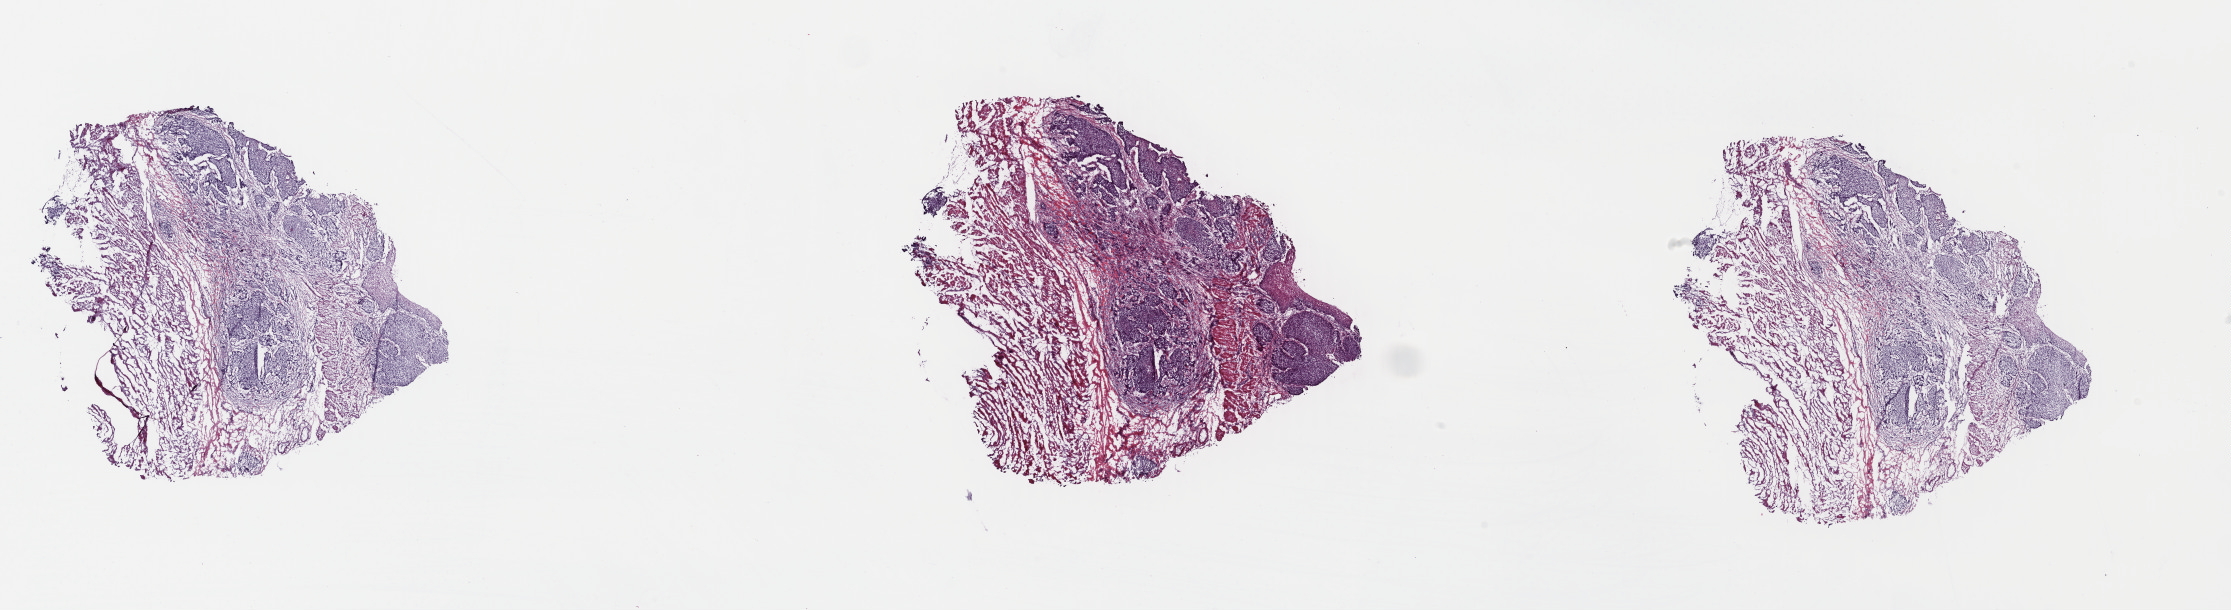
Hematoxylin and eosin (H&E) stained whole-slide image — whole scanned area (about 35.1 x 9.6 mm) shown as a low-resolution overview; frozen section; sample: primary tumour, esophagus. Patient: male, age at initial diagnosis 46 years. Histologic grade: G3 (poorly differentiated). Composition of this section per pathologist review: tumour cells 50%, tumour nuclei 65%, normal cells 50%, stromal cells 0%, necrosis 0%. Infiltration values recorded for this section: lymphocyte infiltration 5%, monocyte infiltration 0%, neutrophil infiltration 0%.
TNM: T3 N1 M0. Pathologic diagnosis: Squamous cell carcinoma, NOS (lower third of esophagus). Lymph nodes positive (case pathology): 2 of 2 examined. AJCC pathologic stage: III (6th edition).